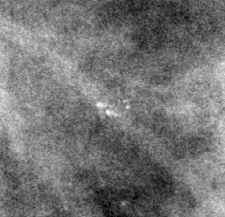
Cropped region of a digitized screen-film mammogram centred on a radiologist-marked abnormality, right breast, CC view, BI-RADS breast density category 3 (scale 1–4).
Finding: calcifications, morphology pleomorphic, distribution clustered; BI-RADS assessment category 4; subtlety rating 3 on a 1 (subtle) to 5 (obvious) scale; pathology result (as recorded, not read from the image): benign.